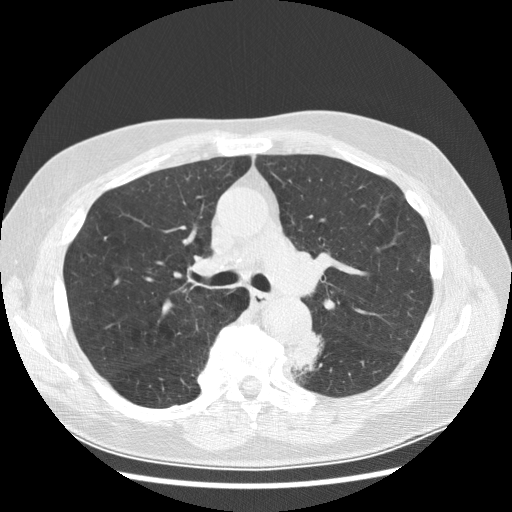
Low-dose screening chest CT, one axial slice. Position 183 of 282 along the scan axis. Reconstruction kernel STANDARD. Lung window (W 1500 / L -600 HU). 512 × 512 image matrix, field of view 370 × 370 mm.
Outlined on this slice (manually delineated by an expert):
- lesion 1 (tumor, lower lobe of left lung): bounding box (x1, y1, x2, y2) in pixels: (294, 331, 324, 376)